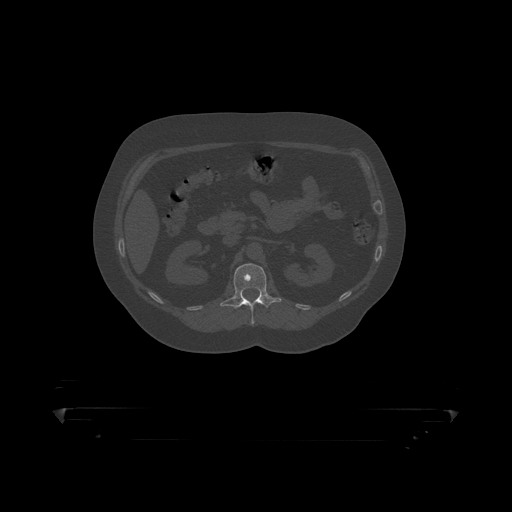
CT including the spine, one axial slice. Slice 149 of 390 in the series (ordered by position). Reconstruction kernel STANDARD. Bone window (W 1800 / L 400 HU). 1.25 mm slice thickness. 512 × 512 image matrix, field of view 650 × 650 mm. Male patient, age 60 years. From the clinical record (not read from this slice): primary cancer: prostate.
Annotated regions visible in this slice (semi-automatic segmentation, software-assisted and operator-edited):
- L1 vertebra: bounding box [x1, y1, x2, y2] px = [220, 264, 282, 319]
- T12 vertebra: [260, 303, 262, 305]